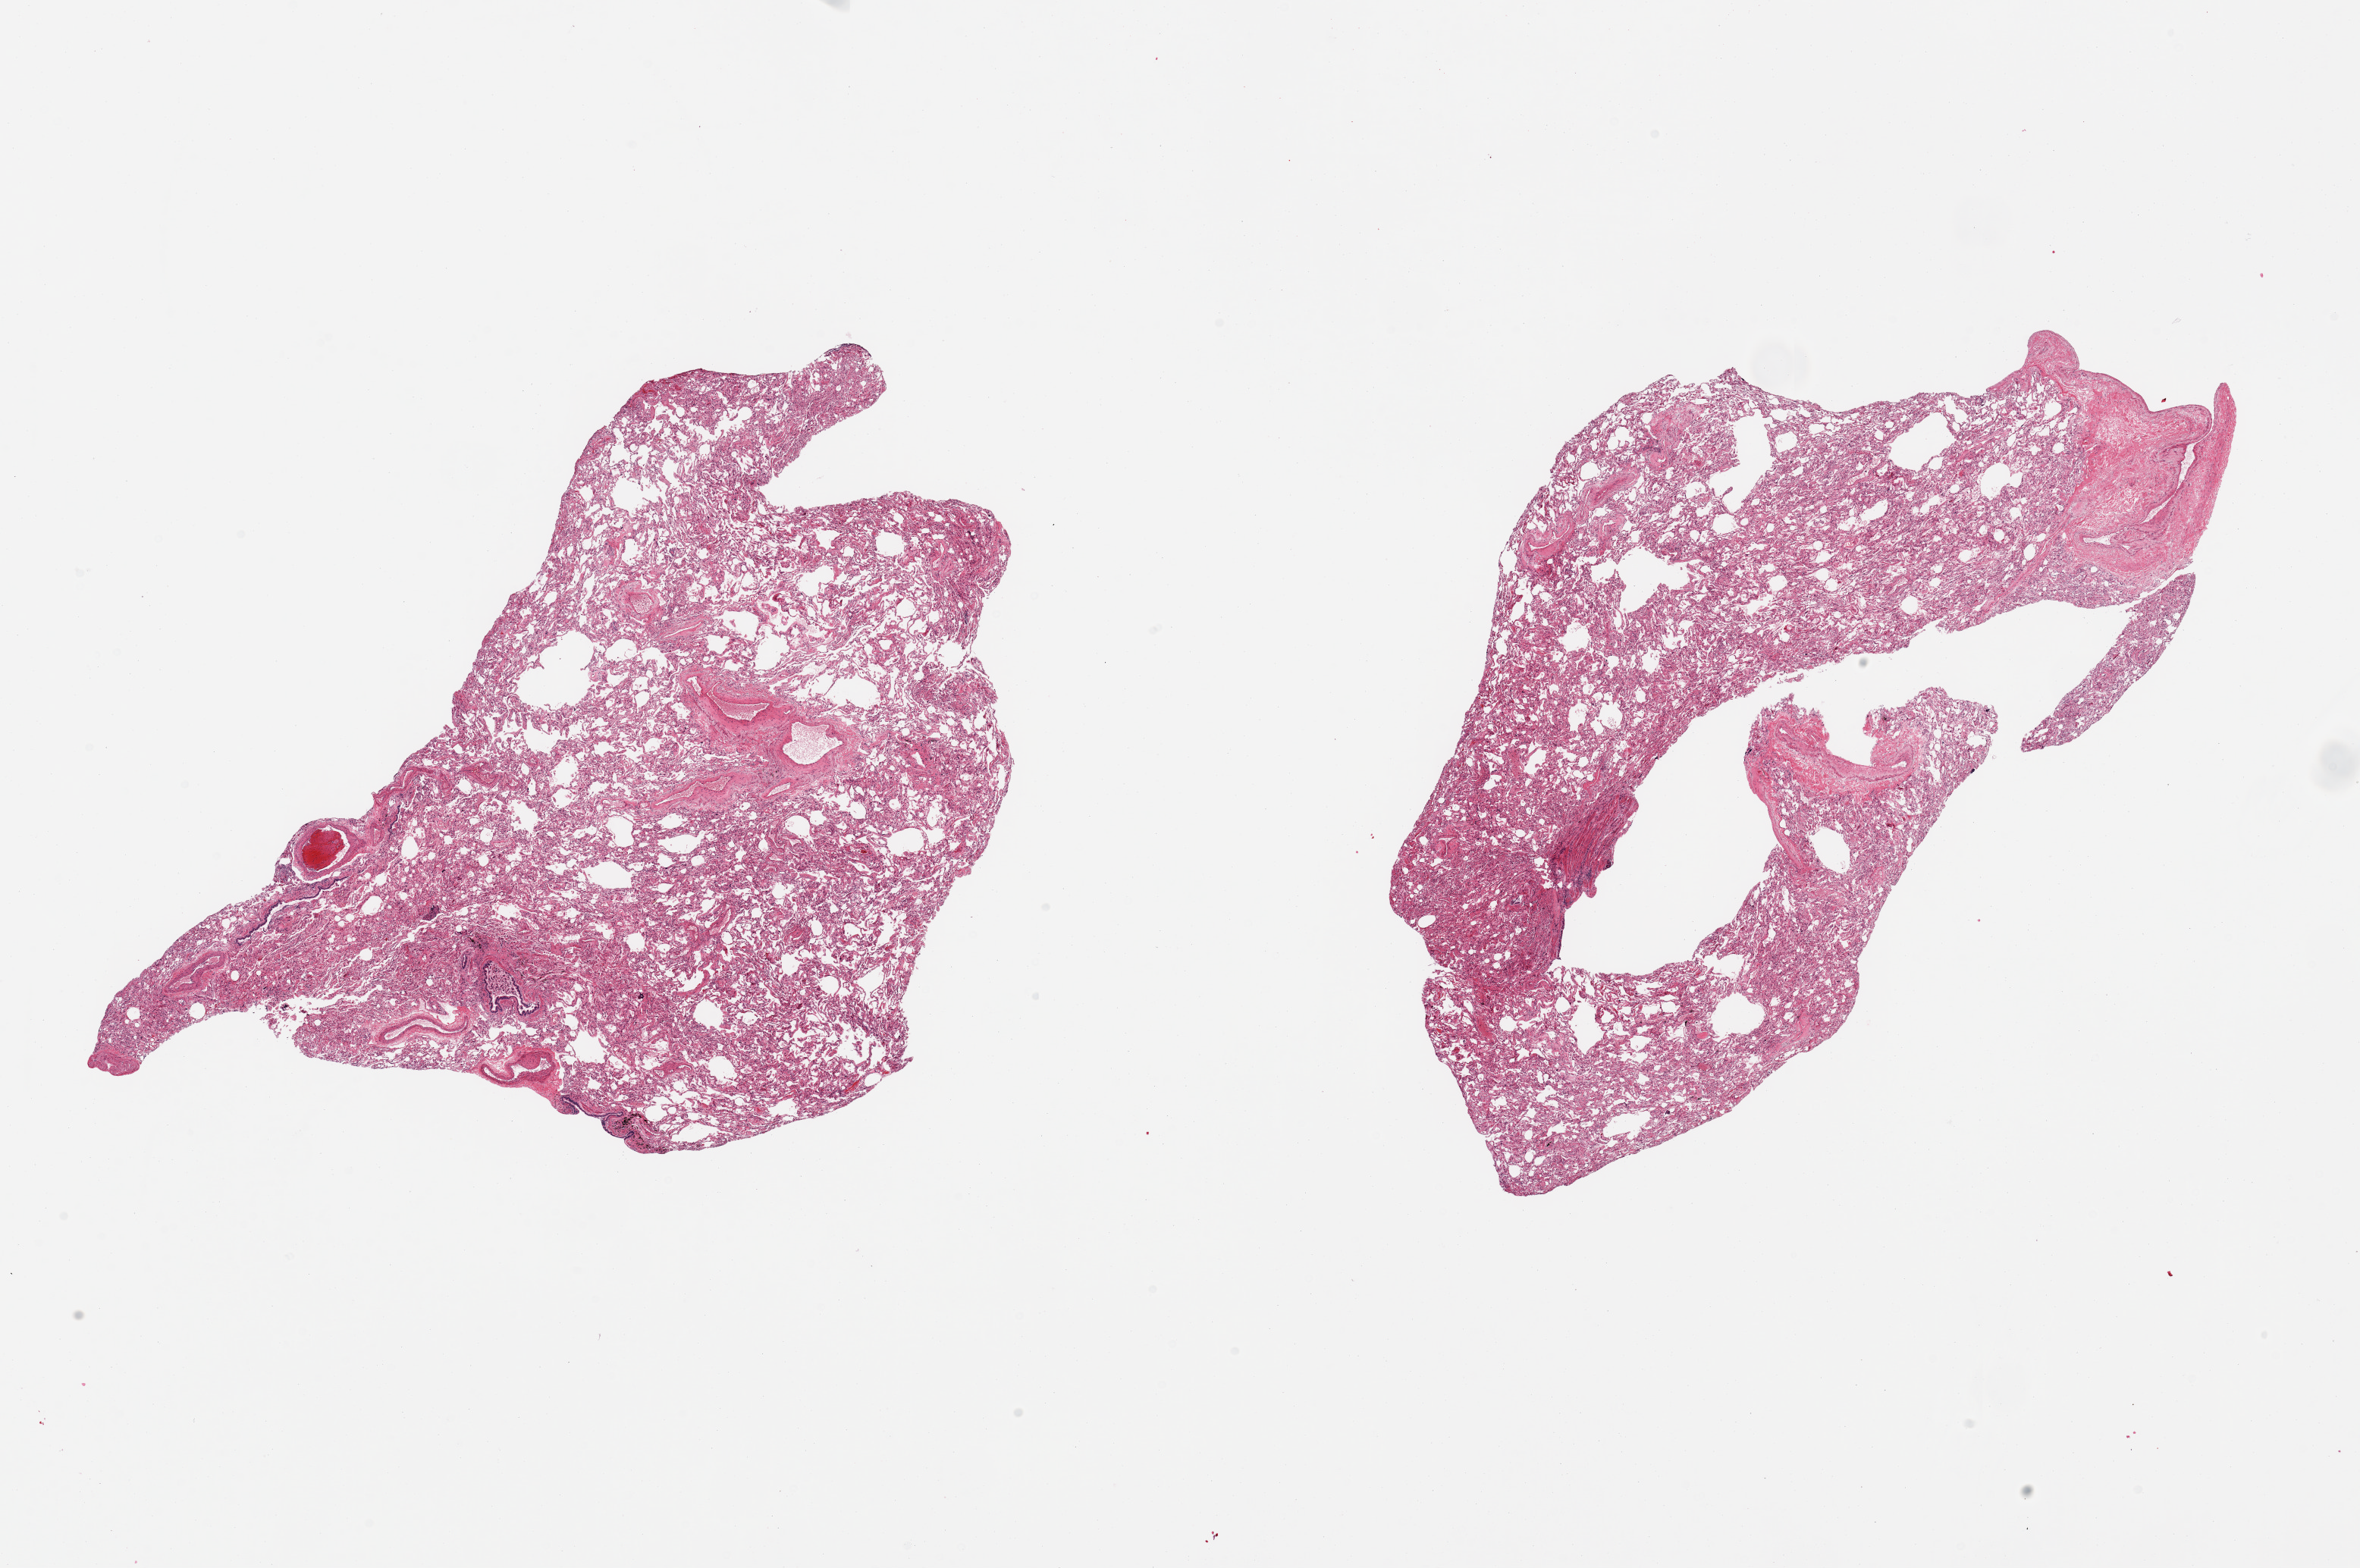
Whole-slide image, H&E stain — low-resolution overview of the scanned area, about 24.6 x 16.4 mm (from a 20x scan), PAXgene-fixed paraffin-embedded (PFPE) section, target tissue: lung, donor tissue sample. Donor: female.
Review note (as recorded): 2 pieces.